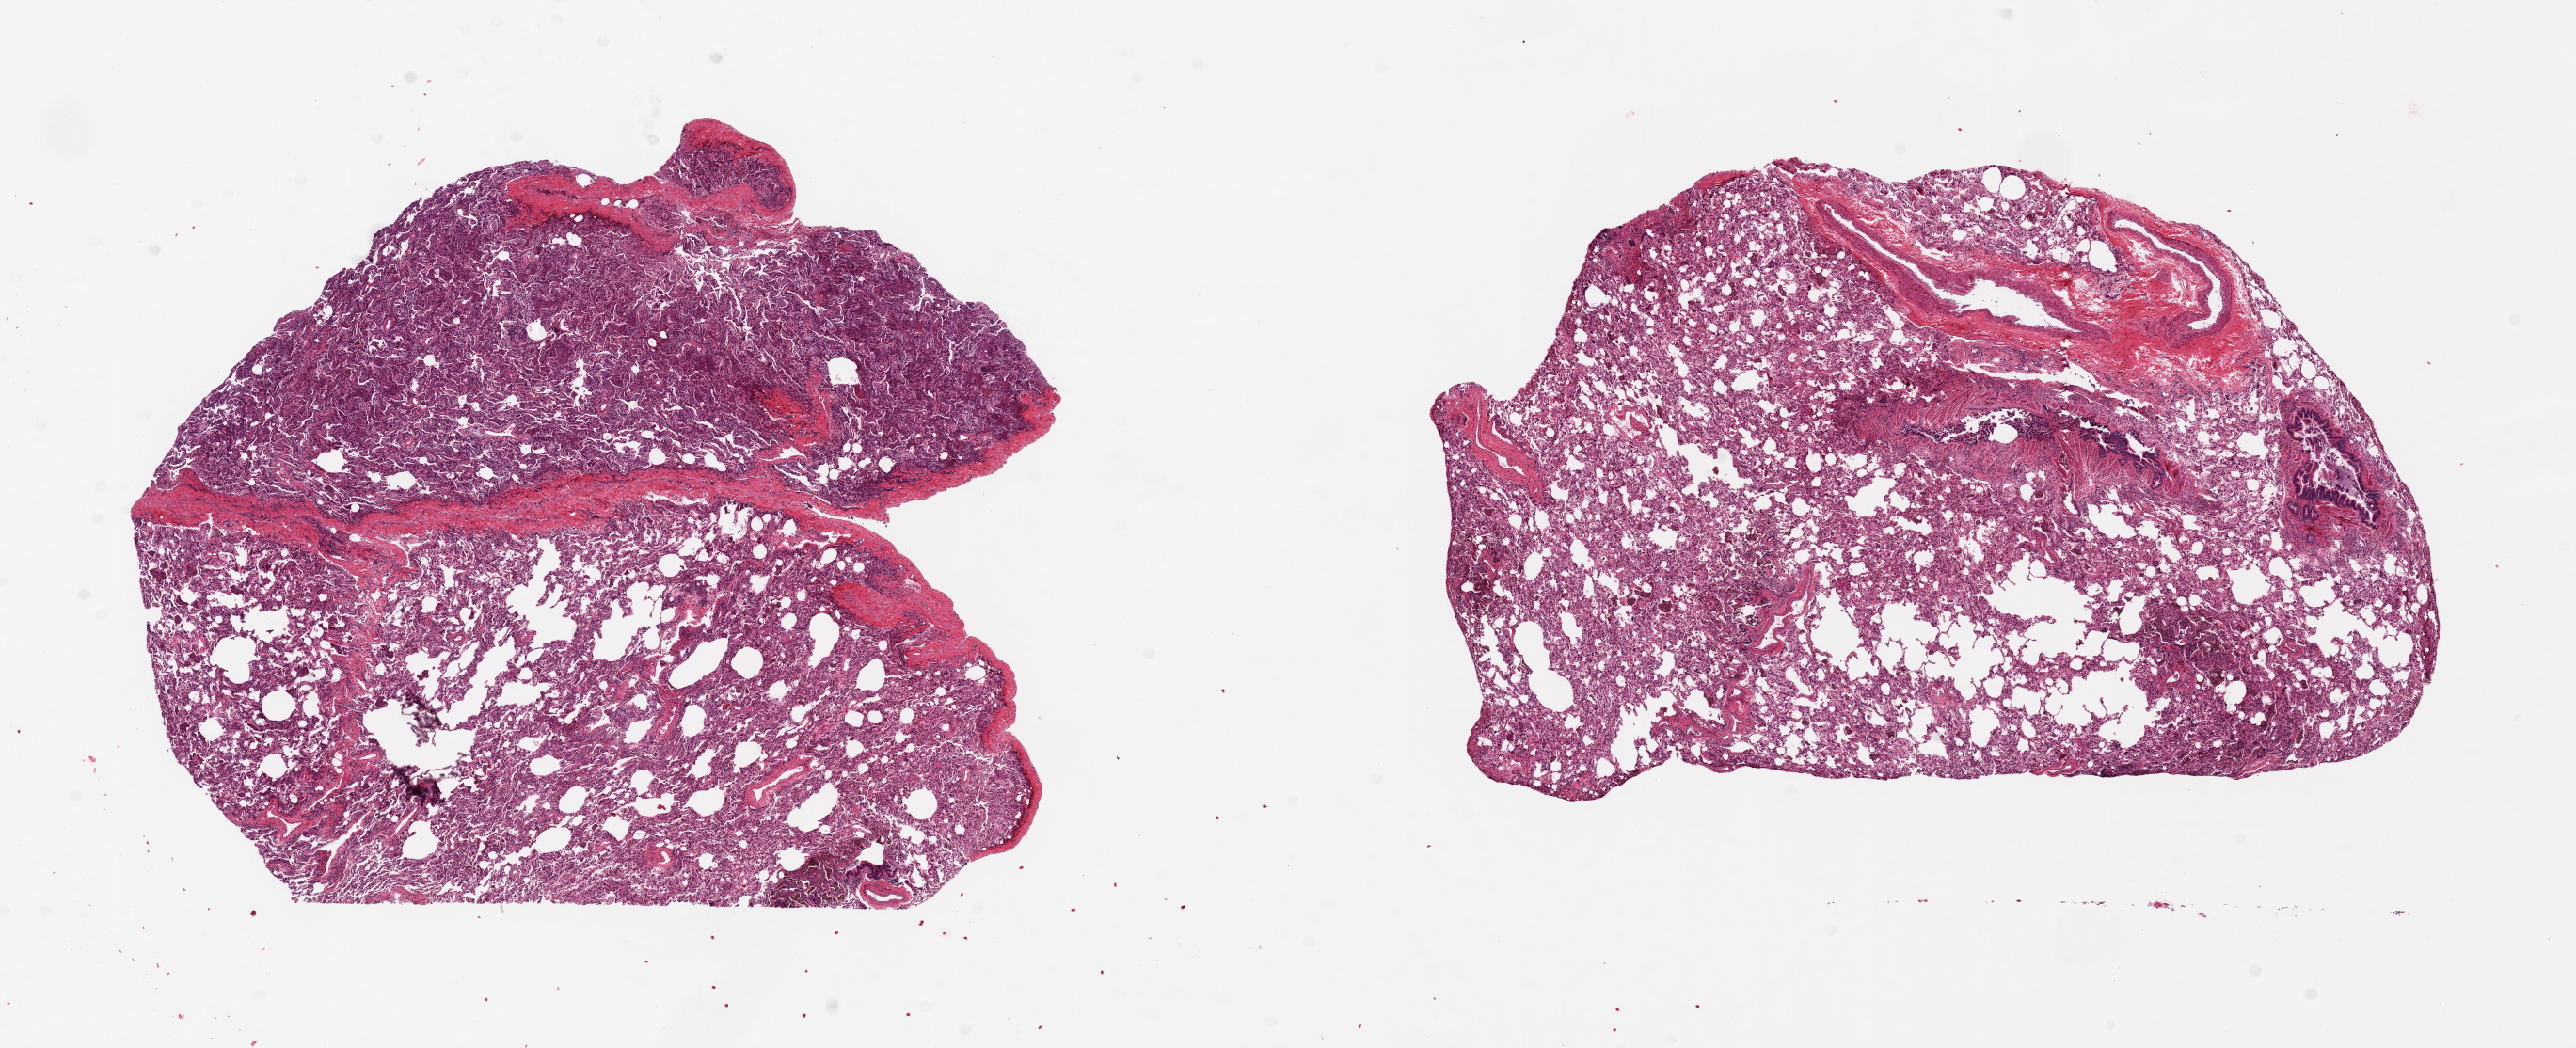
H&E whole-slide image — whole scanned area (about 21.7 x 8.8 mm) shown as a low-resolution overview; PAXgene-fixed, paraffin-embedded tissue; target tissue: lung; donor tissue sample.
Pathologist's review note for this sample: 2 pieces ~7x6, one with marked congestion/chronic pneumonitis.